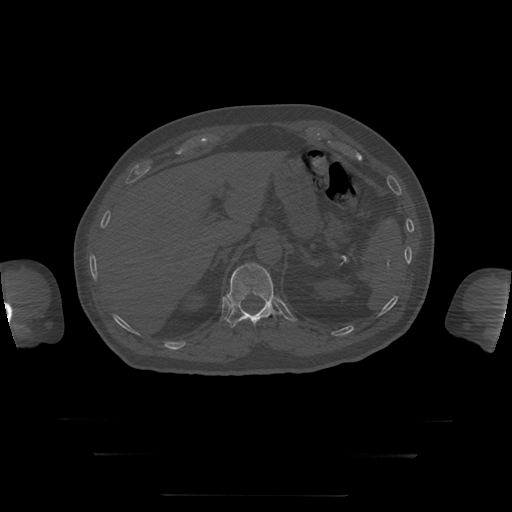
CT including the spine, one axial slice; slice 77 of 397 in the series (ordered by position); reconstruction kernel STANDARD; 120 kVp; bone window (W 1800 / L 400 HU); 1.25 mm slice thickness; 512 × 512 image matrix, field of view 510 × 510 mm. Patient age 73 years. From the clinical record (not read from this slice): primary cancer: prostate.
Annotated regions visible in this slice (semi-automatic segmentation, software-assisted and operator-edited):
- T12 vertebra: box from (x=227, y=263) to (x=282, y=328) px